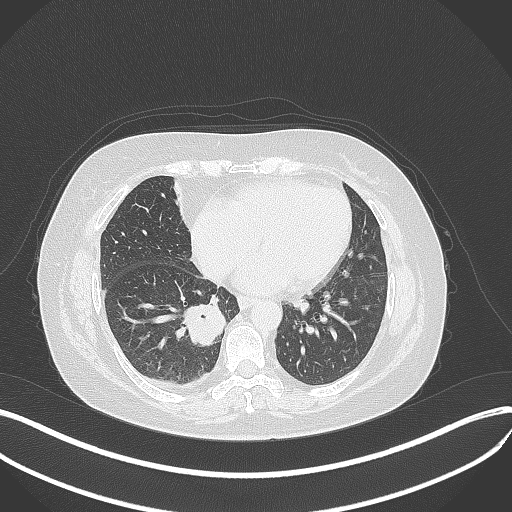
Chest CT, one axial slice; lung window (W 1500 / L -600 HU); 1 mm slice thickness; 512 × 512 image matrix. Patient: female, 56 years. Case-level facts recorded for this patient, not image findings: clinical TNM (as recorded): T2b N1 M0.
Outlined on this slice (rectangle marked by the reading radiologist):
- lung tumour (recorded histology: small cell carcinoma): bounding box (x1, y1, x2, y2) in pixels: (177, 297, 227, 347)